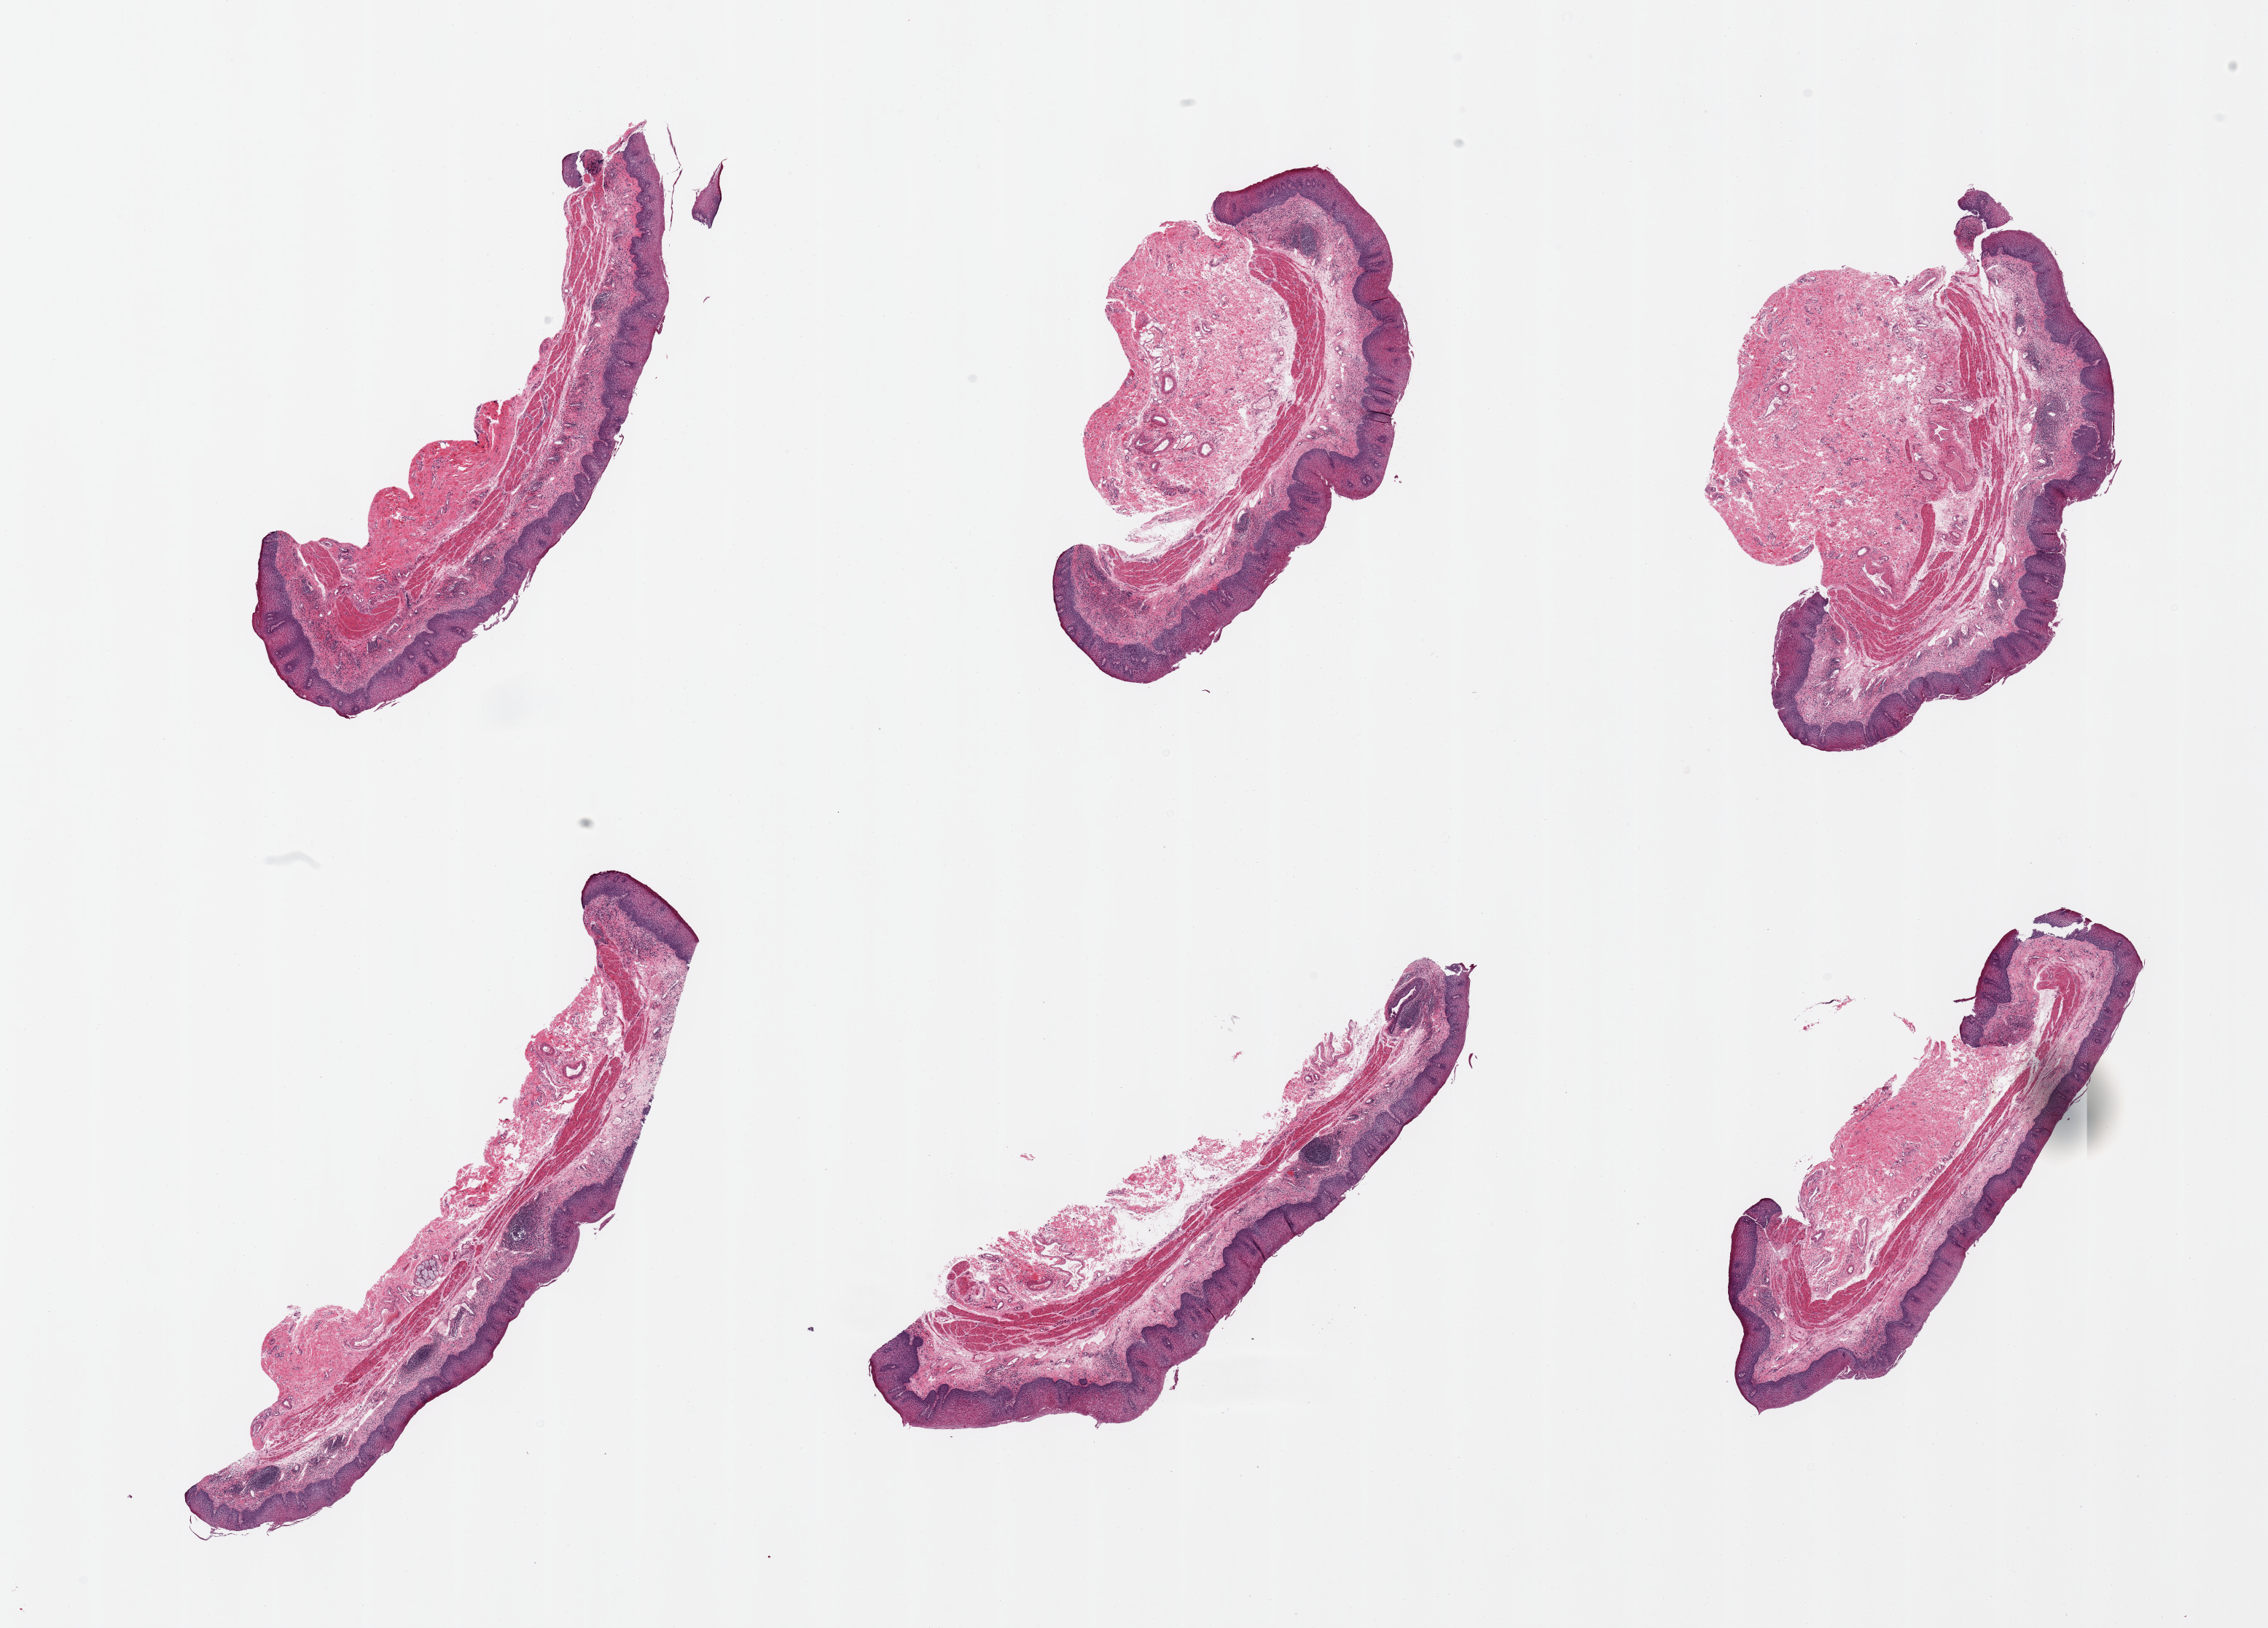
Hematoxylin and eosin (H&E) whole-slide image, brightfield — a low-resolution overview of the entire scanned area, about 24.6 x 17.7 mm (acquisition: 20x scan), PAXgene-fixed paraffin-embedded (PFPE) section, section of esophageal mucous membrane (target tissue), tissue donor sample. Donor: male.
Pathologist's review note for this sample: 6 pieces; esophagitis (c/w reflux) with eosinophilic squamous surface focally.